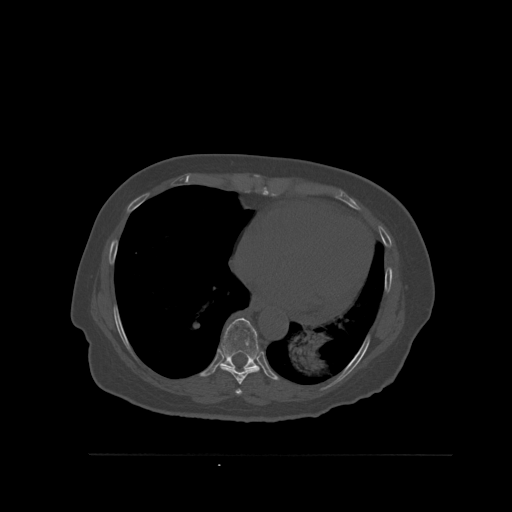
CT including the spine, one axial slice. Bone window (W 1800 / L 400 HU). 1.5 mm slice thickness. 512 × 512 image matrix, field of view 470 × 470 mm. Female patient, age 73 years. From the clinical record (not read from this slice): primary cancer: breast.
Outlined on this slice (semi-automatically segmented with operator editing):
- T7 vertebra: bounding box (x1, y1, x2, y2) in pixels: (235, 389, 242, 395)
- T8 vertebra: (220, 365, 260, 385)
- T9 vertebra: (220, 318, 259, 371)